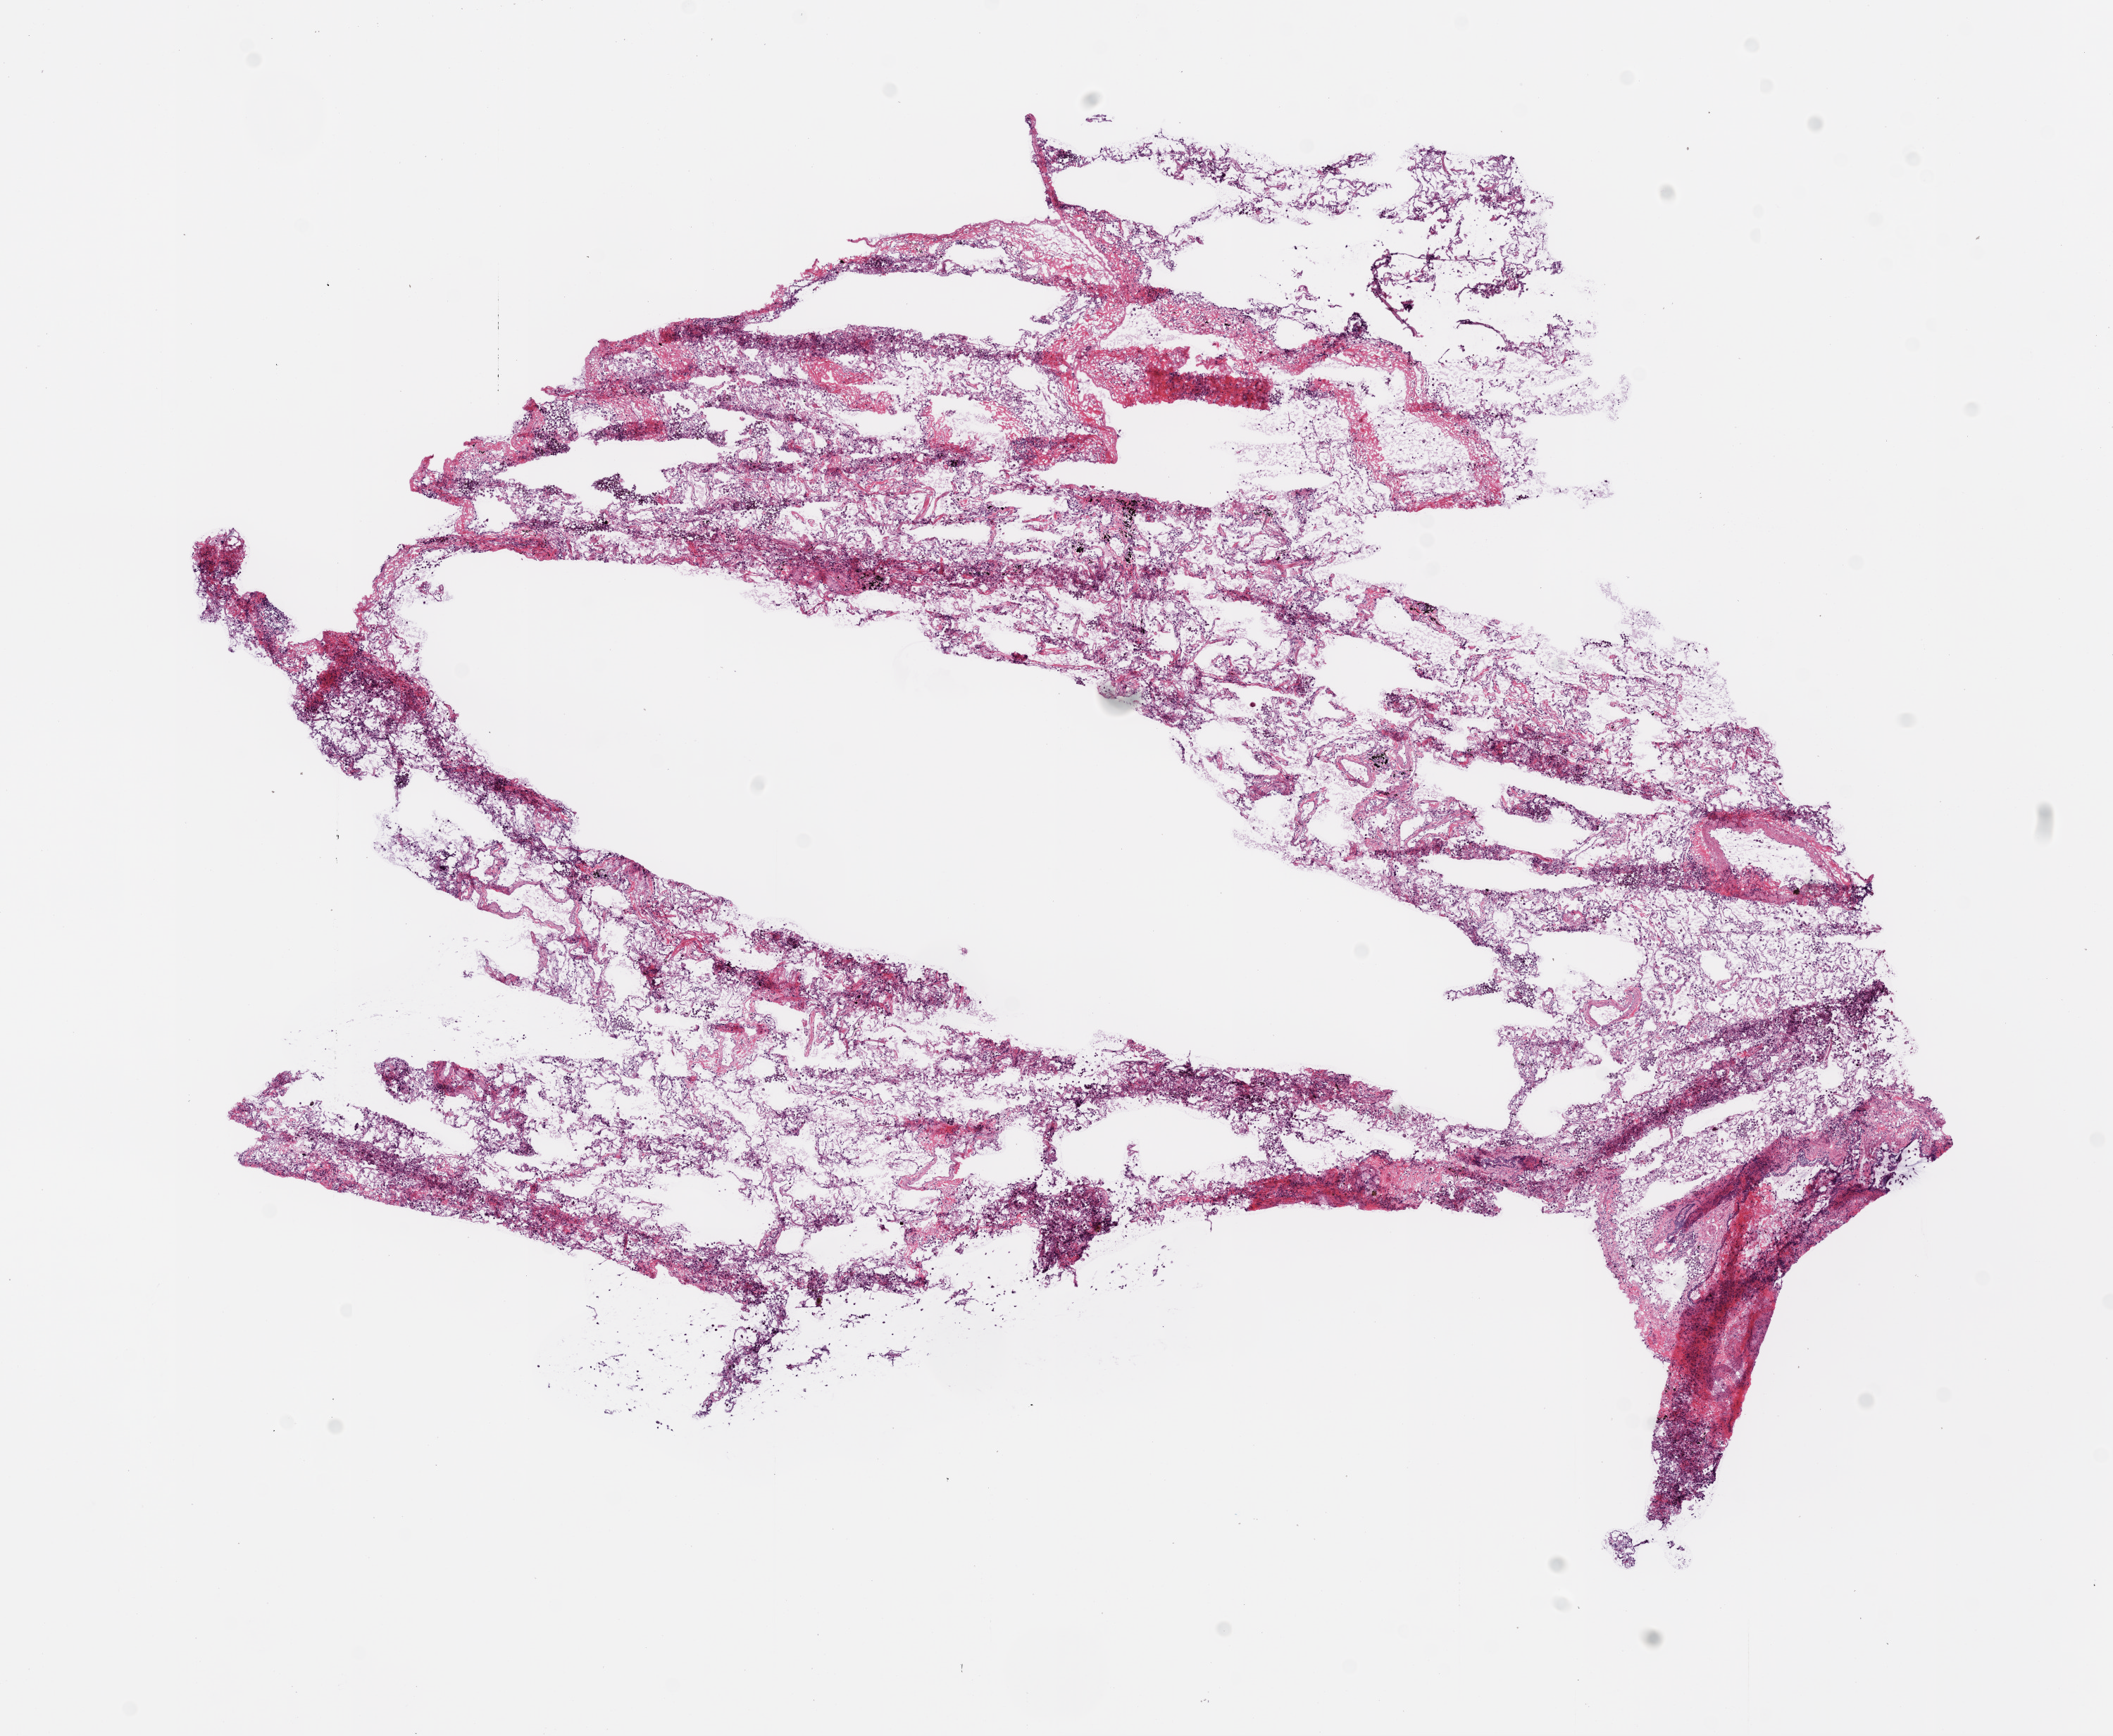
Hematoxylin and eosin (H&E) stained whole-slide image — shown as a low-resolution overview of the whole scanned area (about 12.0 x 9.9 mm, from a 20x scan). Frozen section from the bottom of the tissue portion. Lung, solid tissue normal (non-tumour tissue) sample. Patient: male, age at initial diagnosis 58 years.
This section: solid tissue normal (non-tumour) sample from the same patient. Patient diagnosis: Squamous cell carcinoma, NOS.